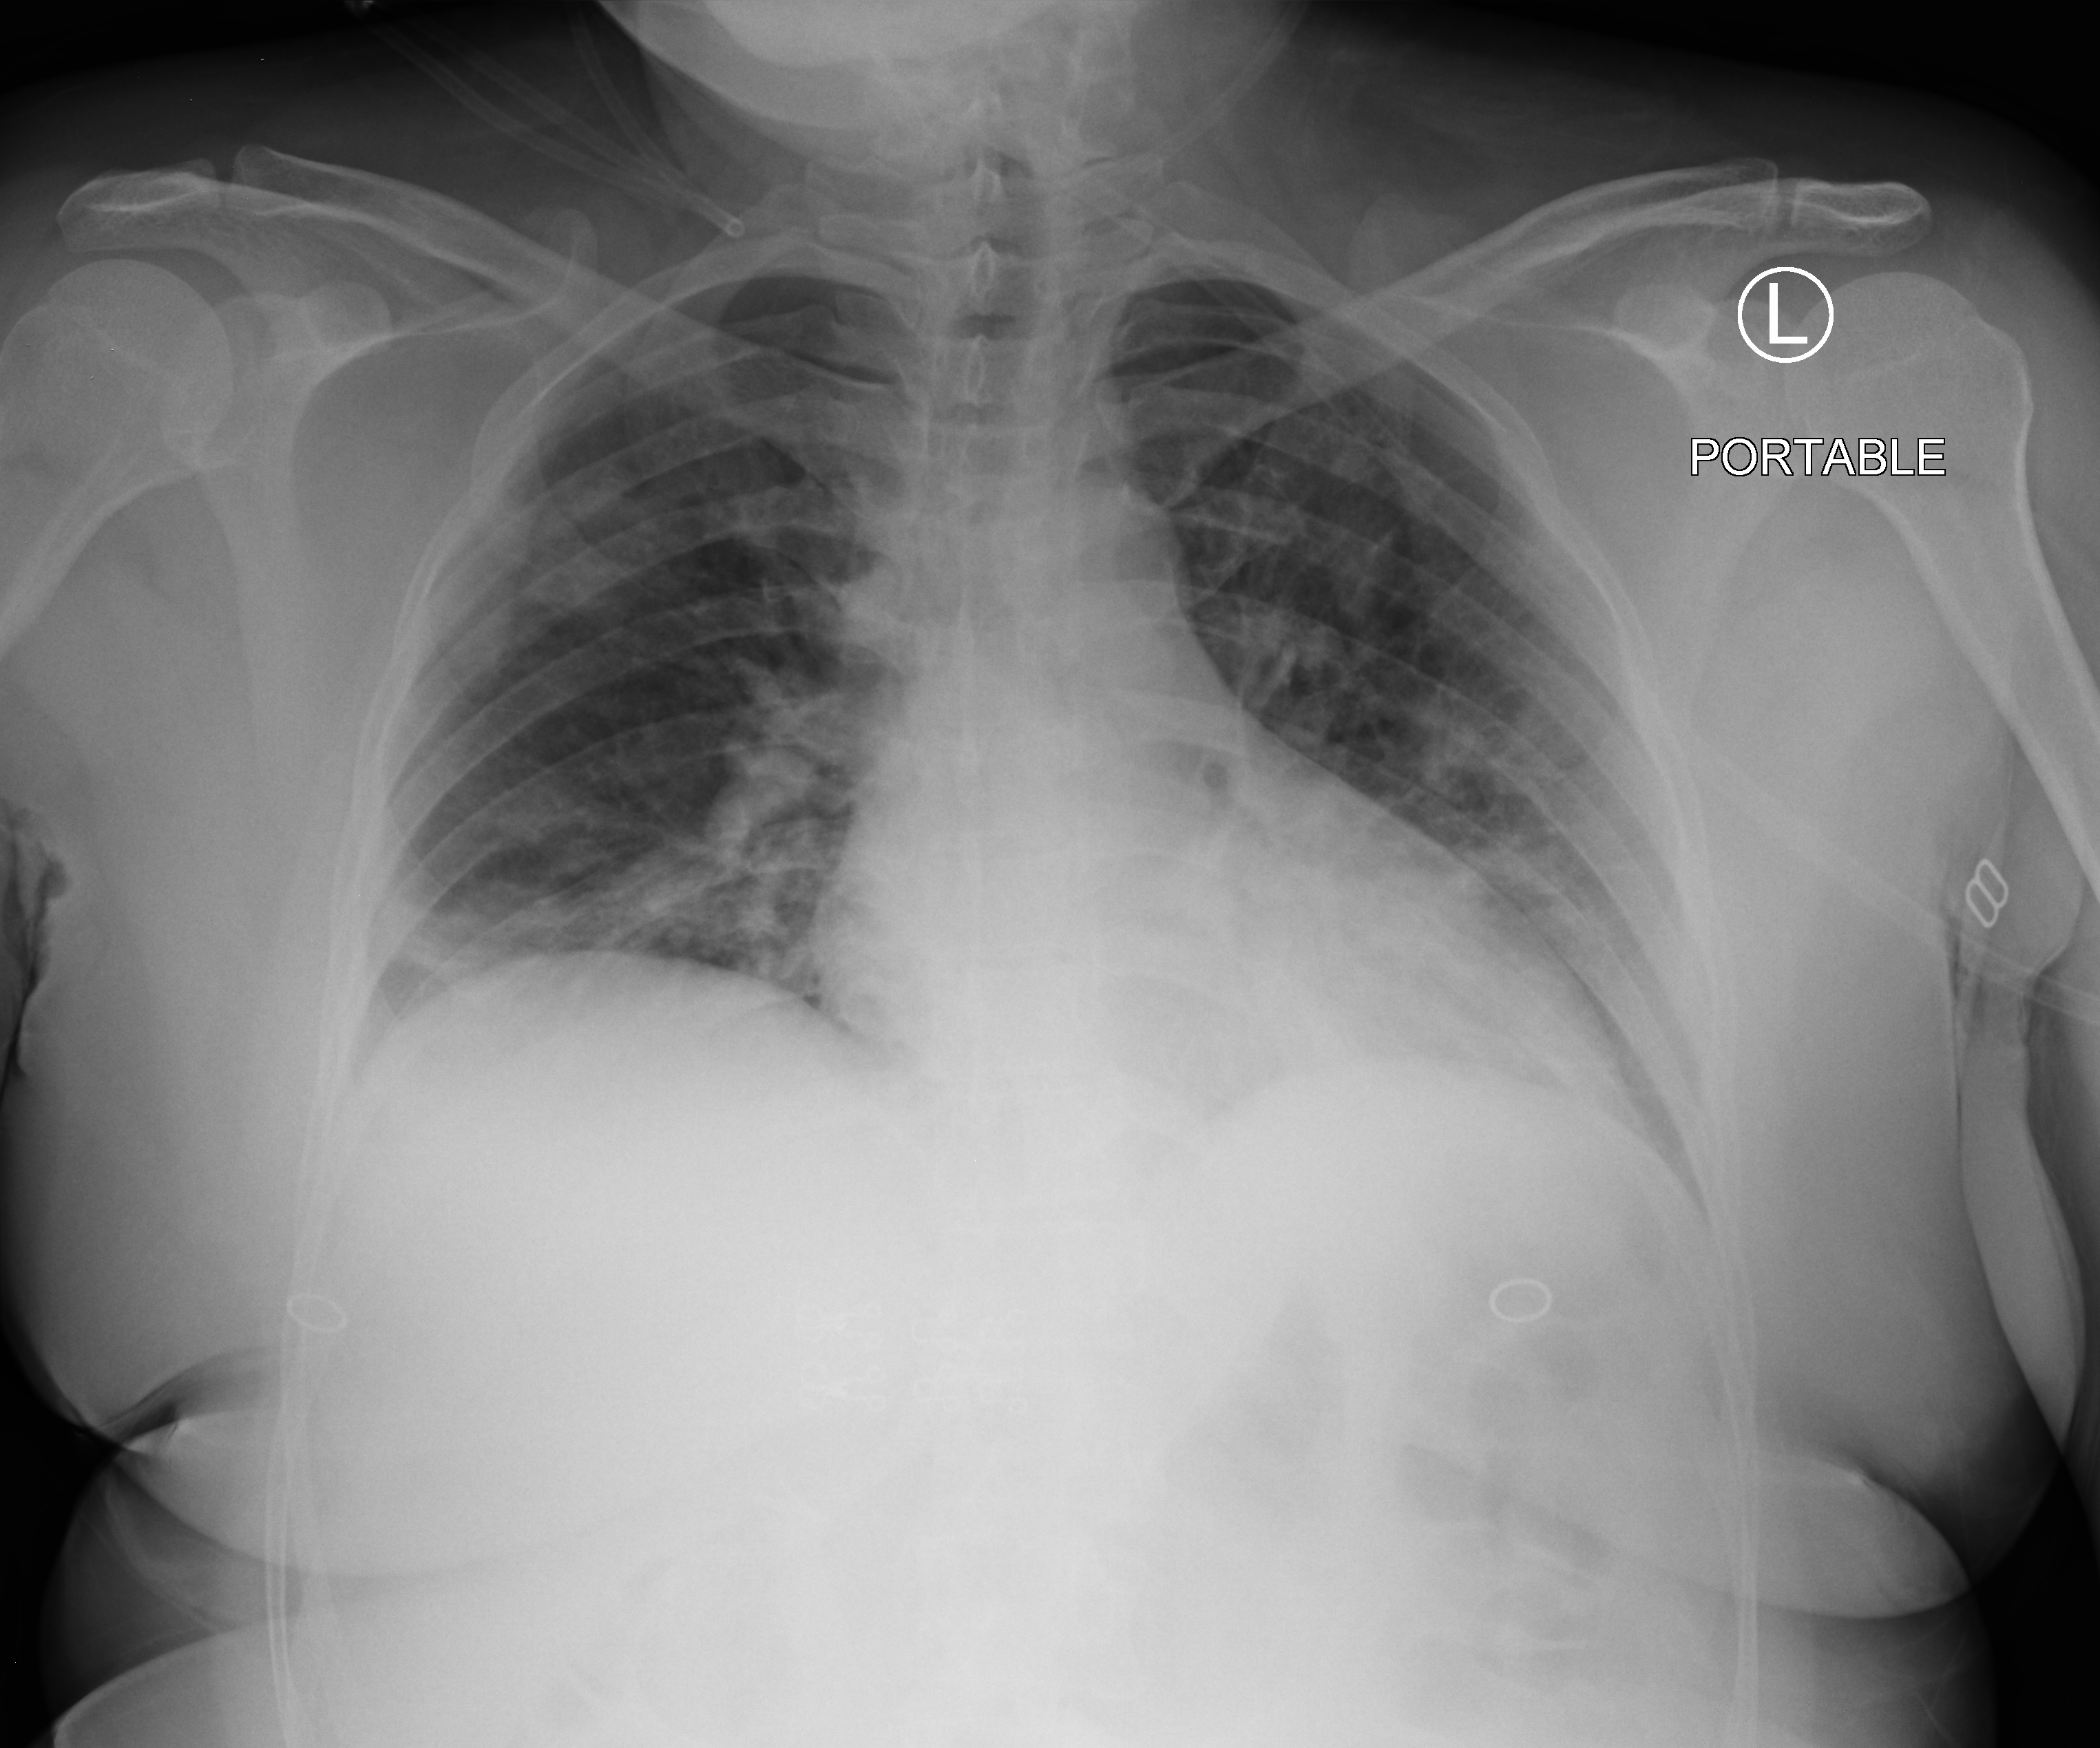
Portable chest radiograph, anteroposterior (AP) projection. Female patient hospitalised with COVID-19, age 18–59 years.
Hospital-stay facts (about this admission, not read from this image; timing relative to this image not recorded): length of hospital stay: 22 days.